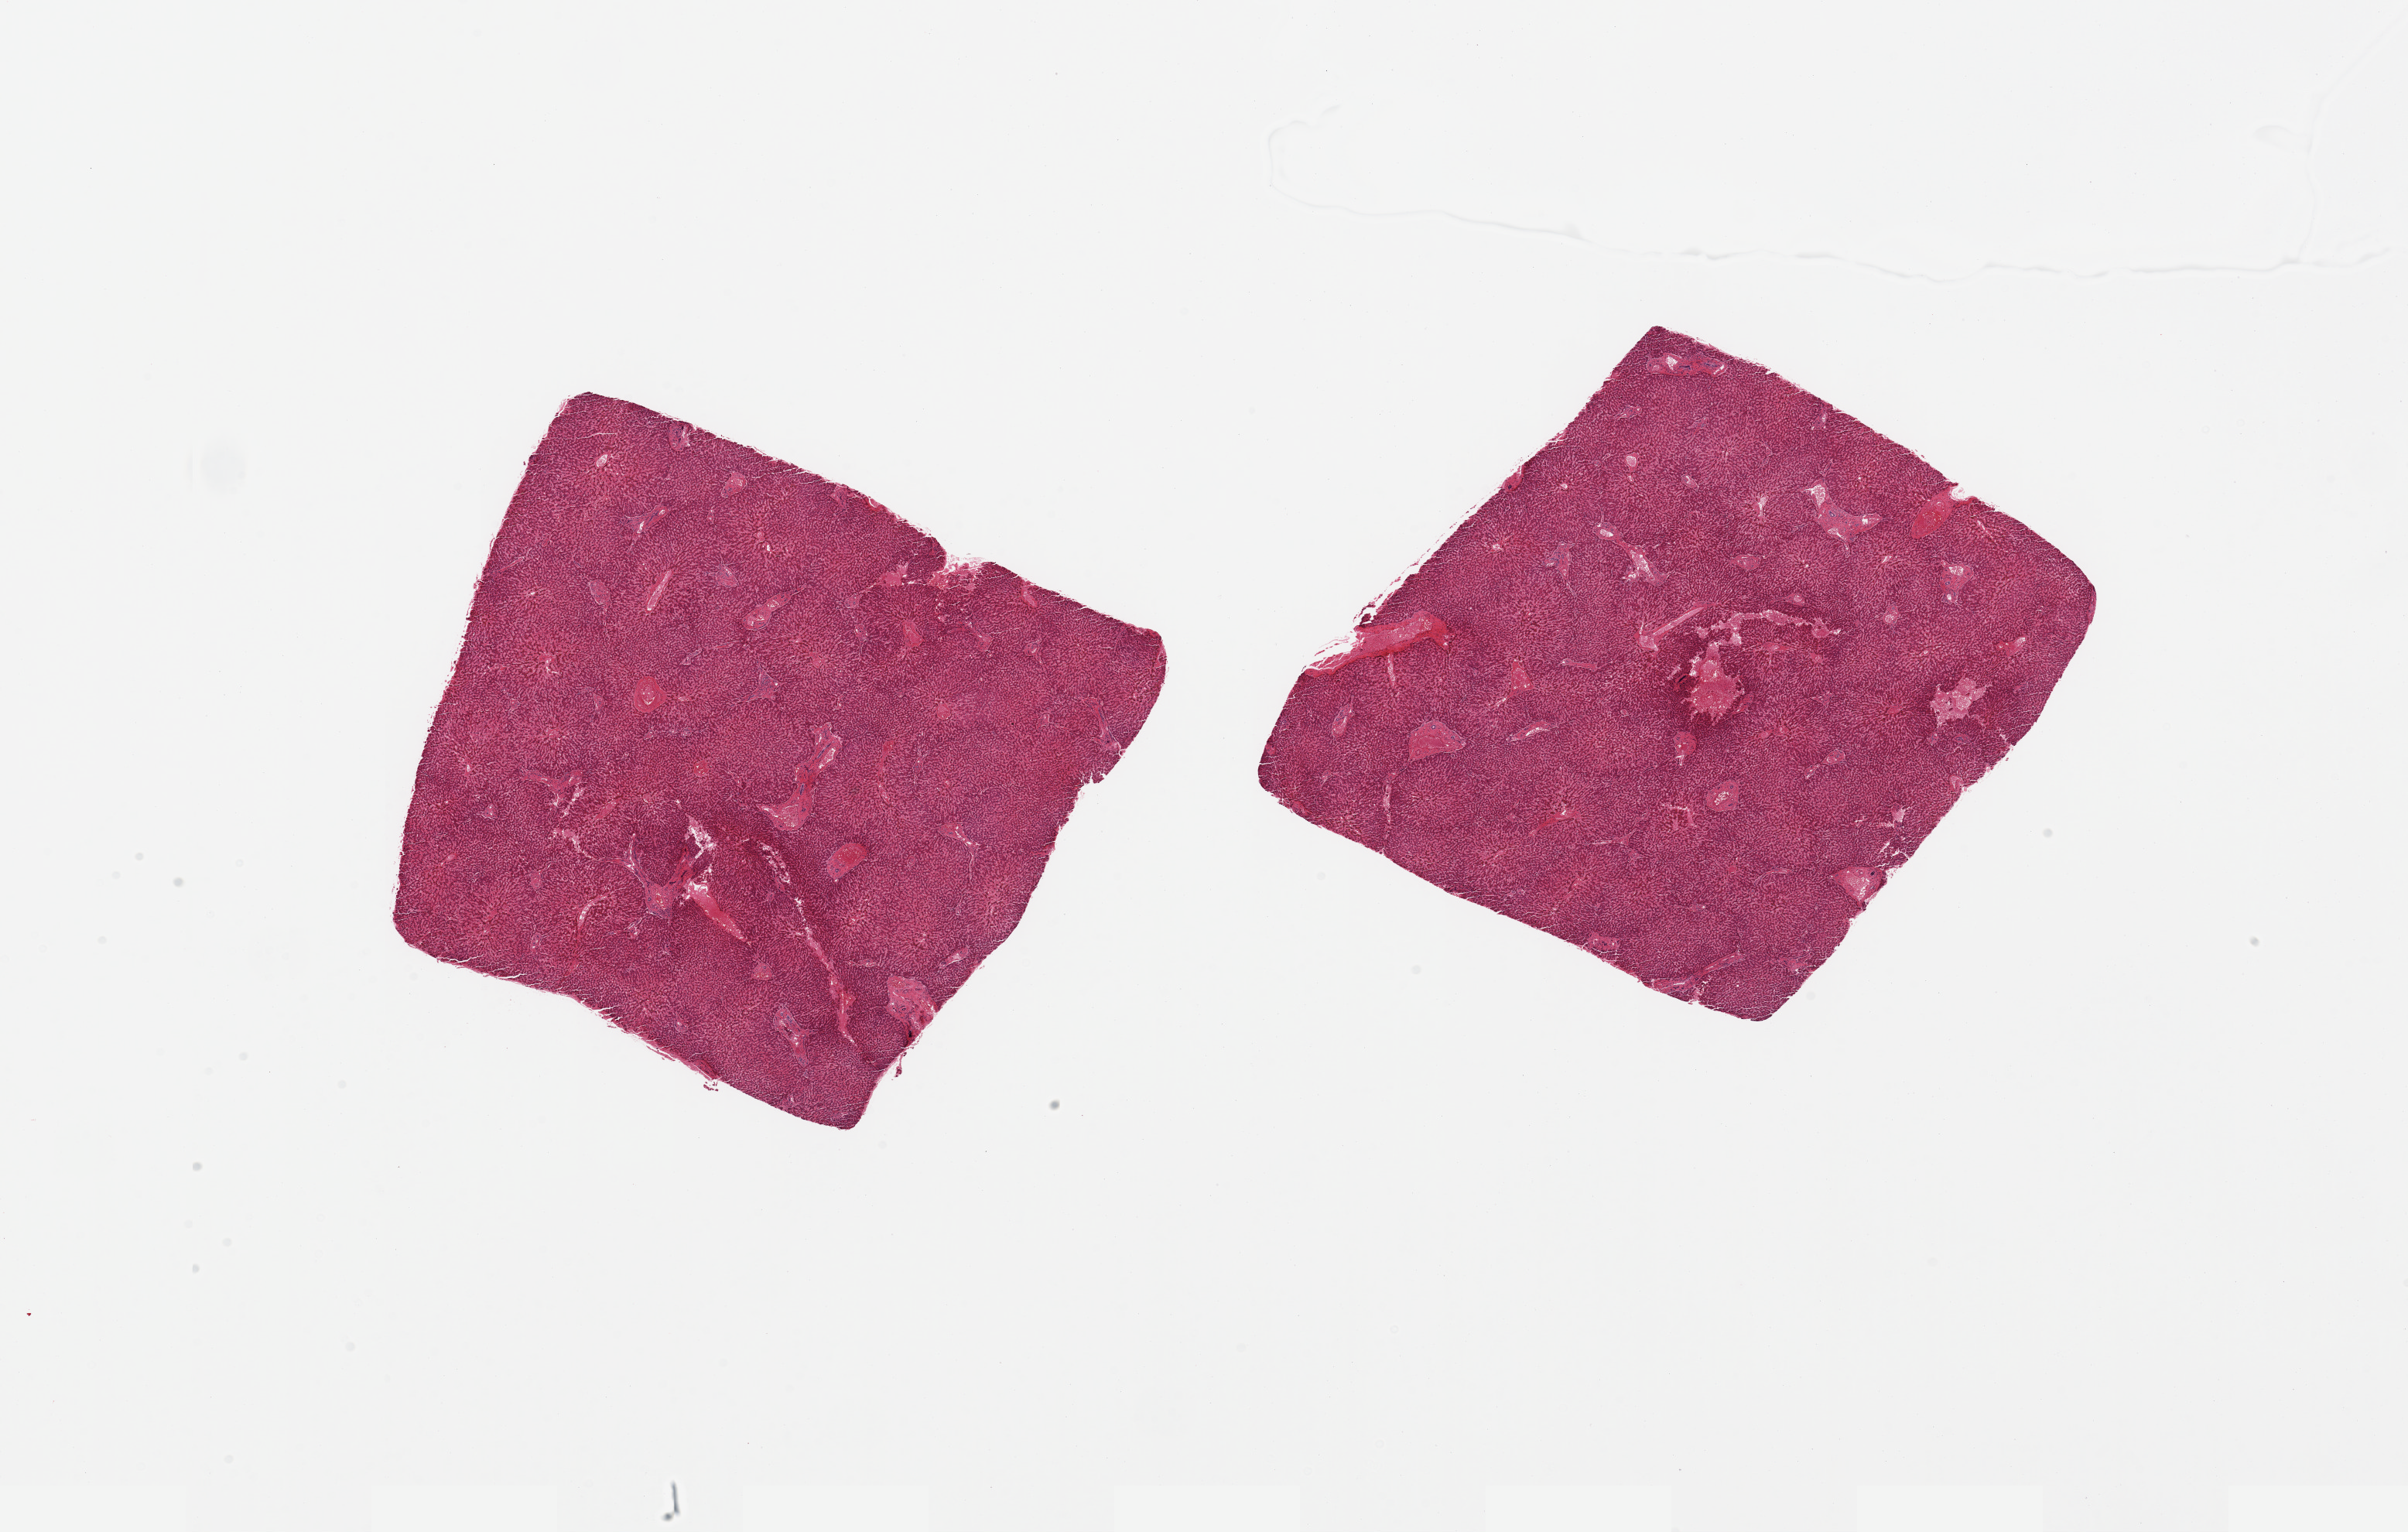
Digitized hematoxylin and eosin (H&E)-stained section — shown as a low-resolution overview of the whole scanned area (about 24.6 x 15.7 mm, from a 20x scan), PAXgene-fixed, paraffin-embedded tissue, sampled site (target tissue): liver, tissue donor sample. Male donor.
Reviewer comment on this tissue sample: 2 pieces; 1 mm focal hemorrhage in 1 piece; venous congestion.